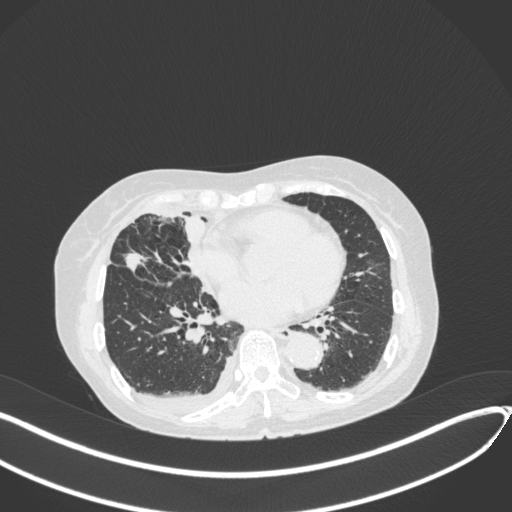
Chest CT, one axial slice; reconstruction kernel B31f; 120 kVp; lung window (W 1500 / L -600 HU); 512 × 512 image matrix. Female patient, age 75 years. Case-level facts recorded for this patient, not image findings: clinical TNM (as recorded): T2a N3 M0.
Annotated regions visible in this slice (rectangle marked by the reading radiologist):
- lung tumour (recorded histology: adenocarcinoma): box from (x=119, y=250) to (x=145, y=277) px